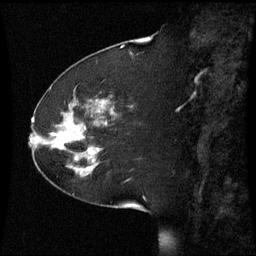
Breast MRI (dynamic contrast-enhanced), one sagittal slice; position 22 of 60 along the scan axis; dynamic contrast-enhanced series, image 2 of 3 at this slice position (ordered by acquisition); 1.5 T; TE 4.2 ms, TR 8.9 ms; 2.2 mm slice thickness; 256 × 256 image matrix, field of view 220 × 220 mm. Patient: female, 51 years. Case-level facts recorded for this patient, not image findings: setting: breast cancer imaged before/during neoadjuvant chemotherapy; receptor status: HR-positive, HER2-negative.
Annotated regions visible in this slice (semi-automatic segmentation, software-assisted and operator-edited):
- analysis volume of interest (the breast-tissue region the enhancement analysis was run in; not a lesion): bounding box (x1, y1, x2, y2) in pixels: (44, 102, 109, 169)
- tumour enhancement mask (voxels above the 70 % enhancement threshold inside the analysis volume of interest): (52, 124, 75, 147)